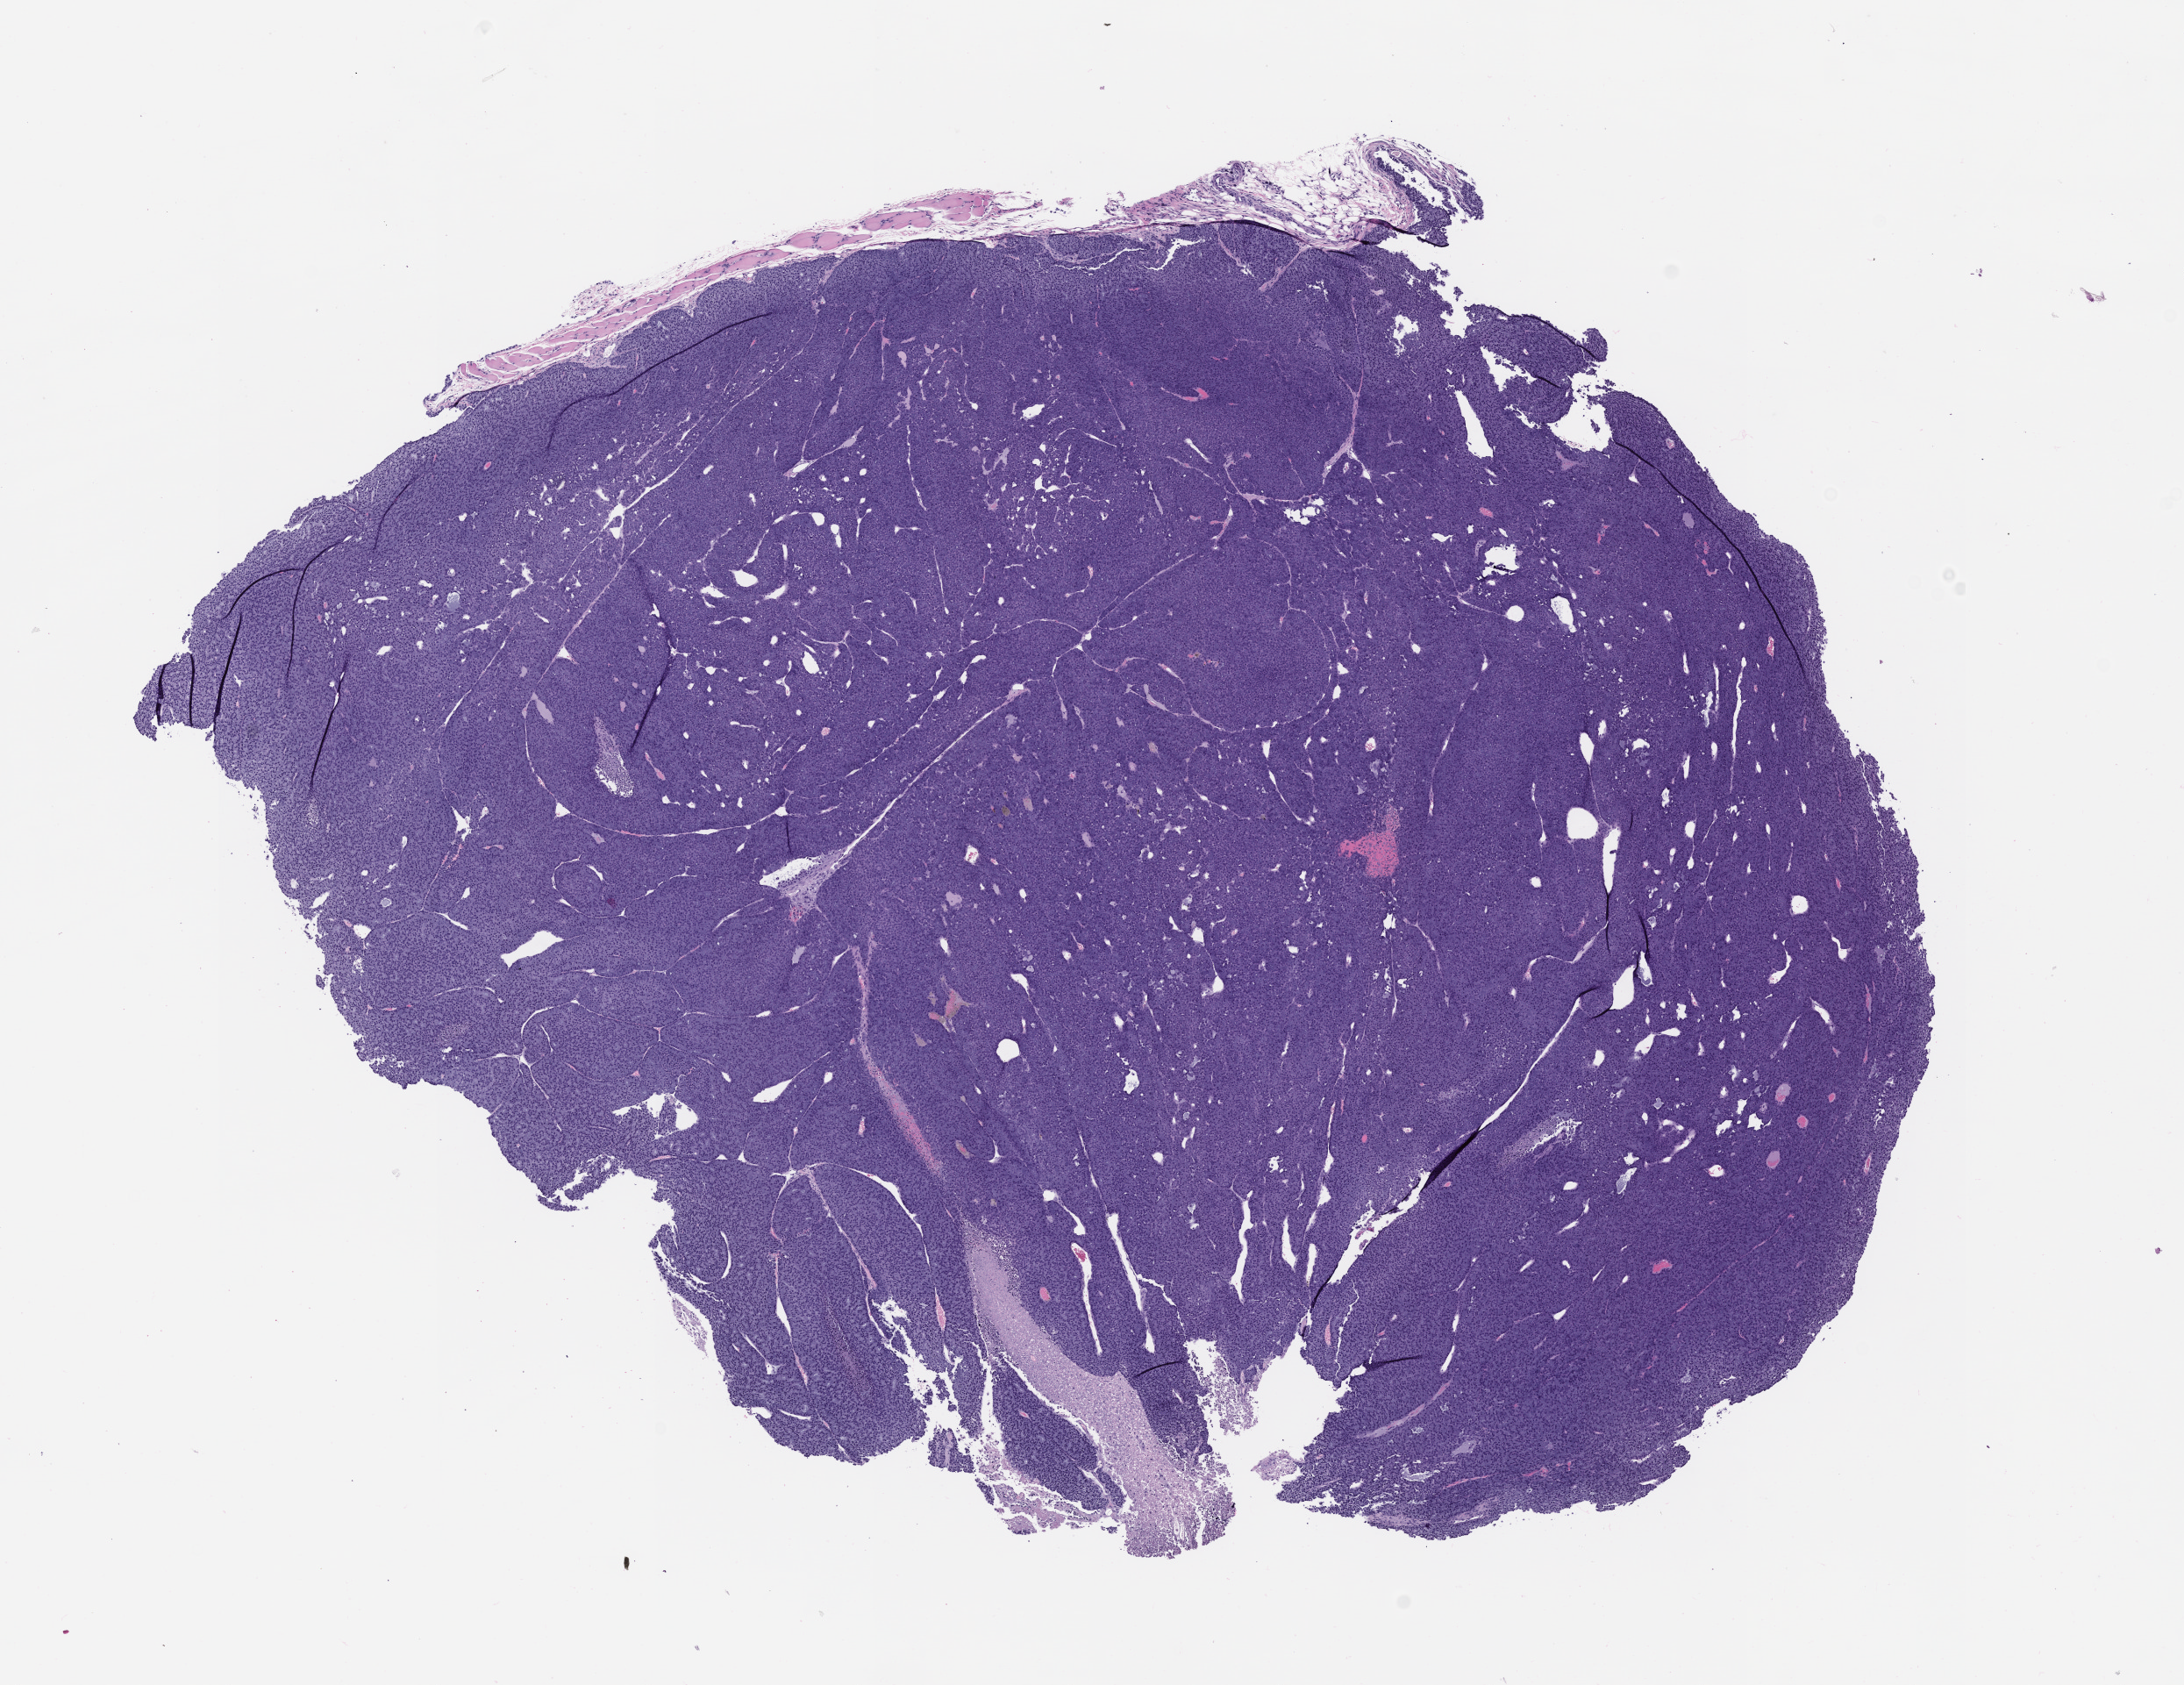
Whole-slide image, hematoxylin and eosin (H&E): patient-derived xenograft (human tumor grown in a mouse), passage 2, low-resolution overview of the scanned area, about 10.0 x 7.7 mm, FFPE section, tumor site category: head and neck.
Originating patient diagnosis: Acinar Cell Carcinoma.